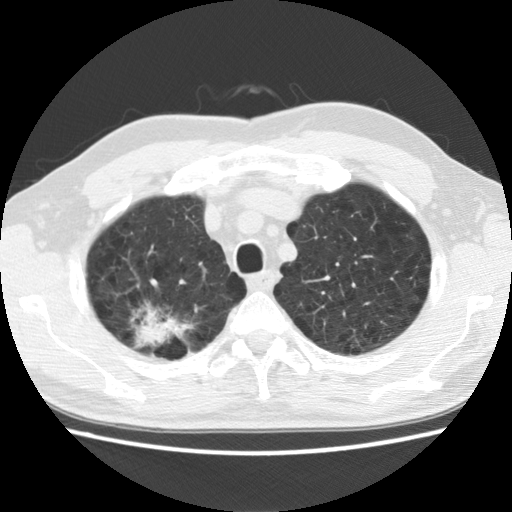
Axial slice from a low-dose chest CT screening exam, baseline screening round, lung window (W 1500 / L -600 HU), standard (soft-tissue) reconstruction kernel (STANDARD), 512 × 512 image matrix, field of view 340 × 340 mm. Male, age 64 years at enrolment. Former smoker at enrolment.
- Expert-annotated lung lesion, bounding box <111,291,200,363> (left, top, right, bottom; pixels).
- Reader record for this screening exam (exam-level; its link to the box is not recorded): non-calcified nodule or mass ≥4 mm, right upper lobe, 39 × 31 mm, spiculated (stellate) margins, mixed attenuation.
- Official screen result: positive, change unspecified: nodule(s) >= 4 mm or enlarging nodule(s), mass(es), or other non-specific abnormalities suspicious for lung cancer.